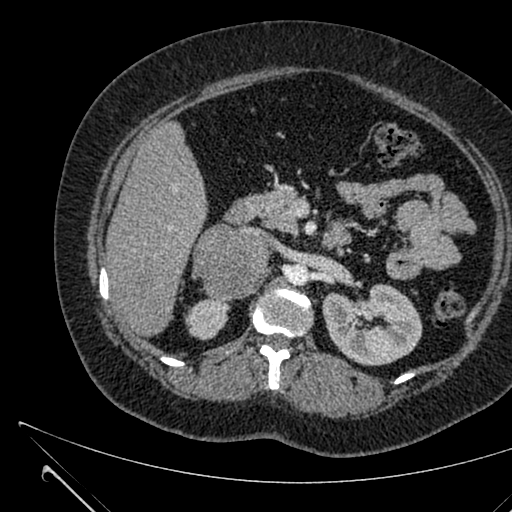
Contrast-enhanced abdominal CT, one axial slice; slice 380 of 731 in the series (ordered by position); 120 kVp; intravenous contrast given; soft-tissue window (W 400 / L 40 HU); 1 mm slice thickness; 512 × 512 image matrix, field of view 376 × 376 mm. Female patient, age 36 years. From the clinical record (not read from this slice): diagnosis: adrenocortical carcinoma; tumour side: right adrenal; tumour size at pathology: 10 cm; Ki-67 index: 20 %; stage (as recorded): 4.
Structures marked on this image (semi-automatically segmented with operator editing):
- mass: bounding box (x1, y1, x2, y2) in pixels: (193, 223, 269, 300)